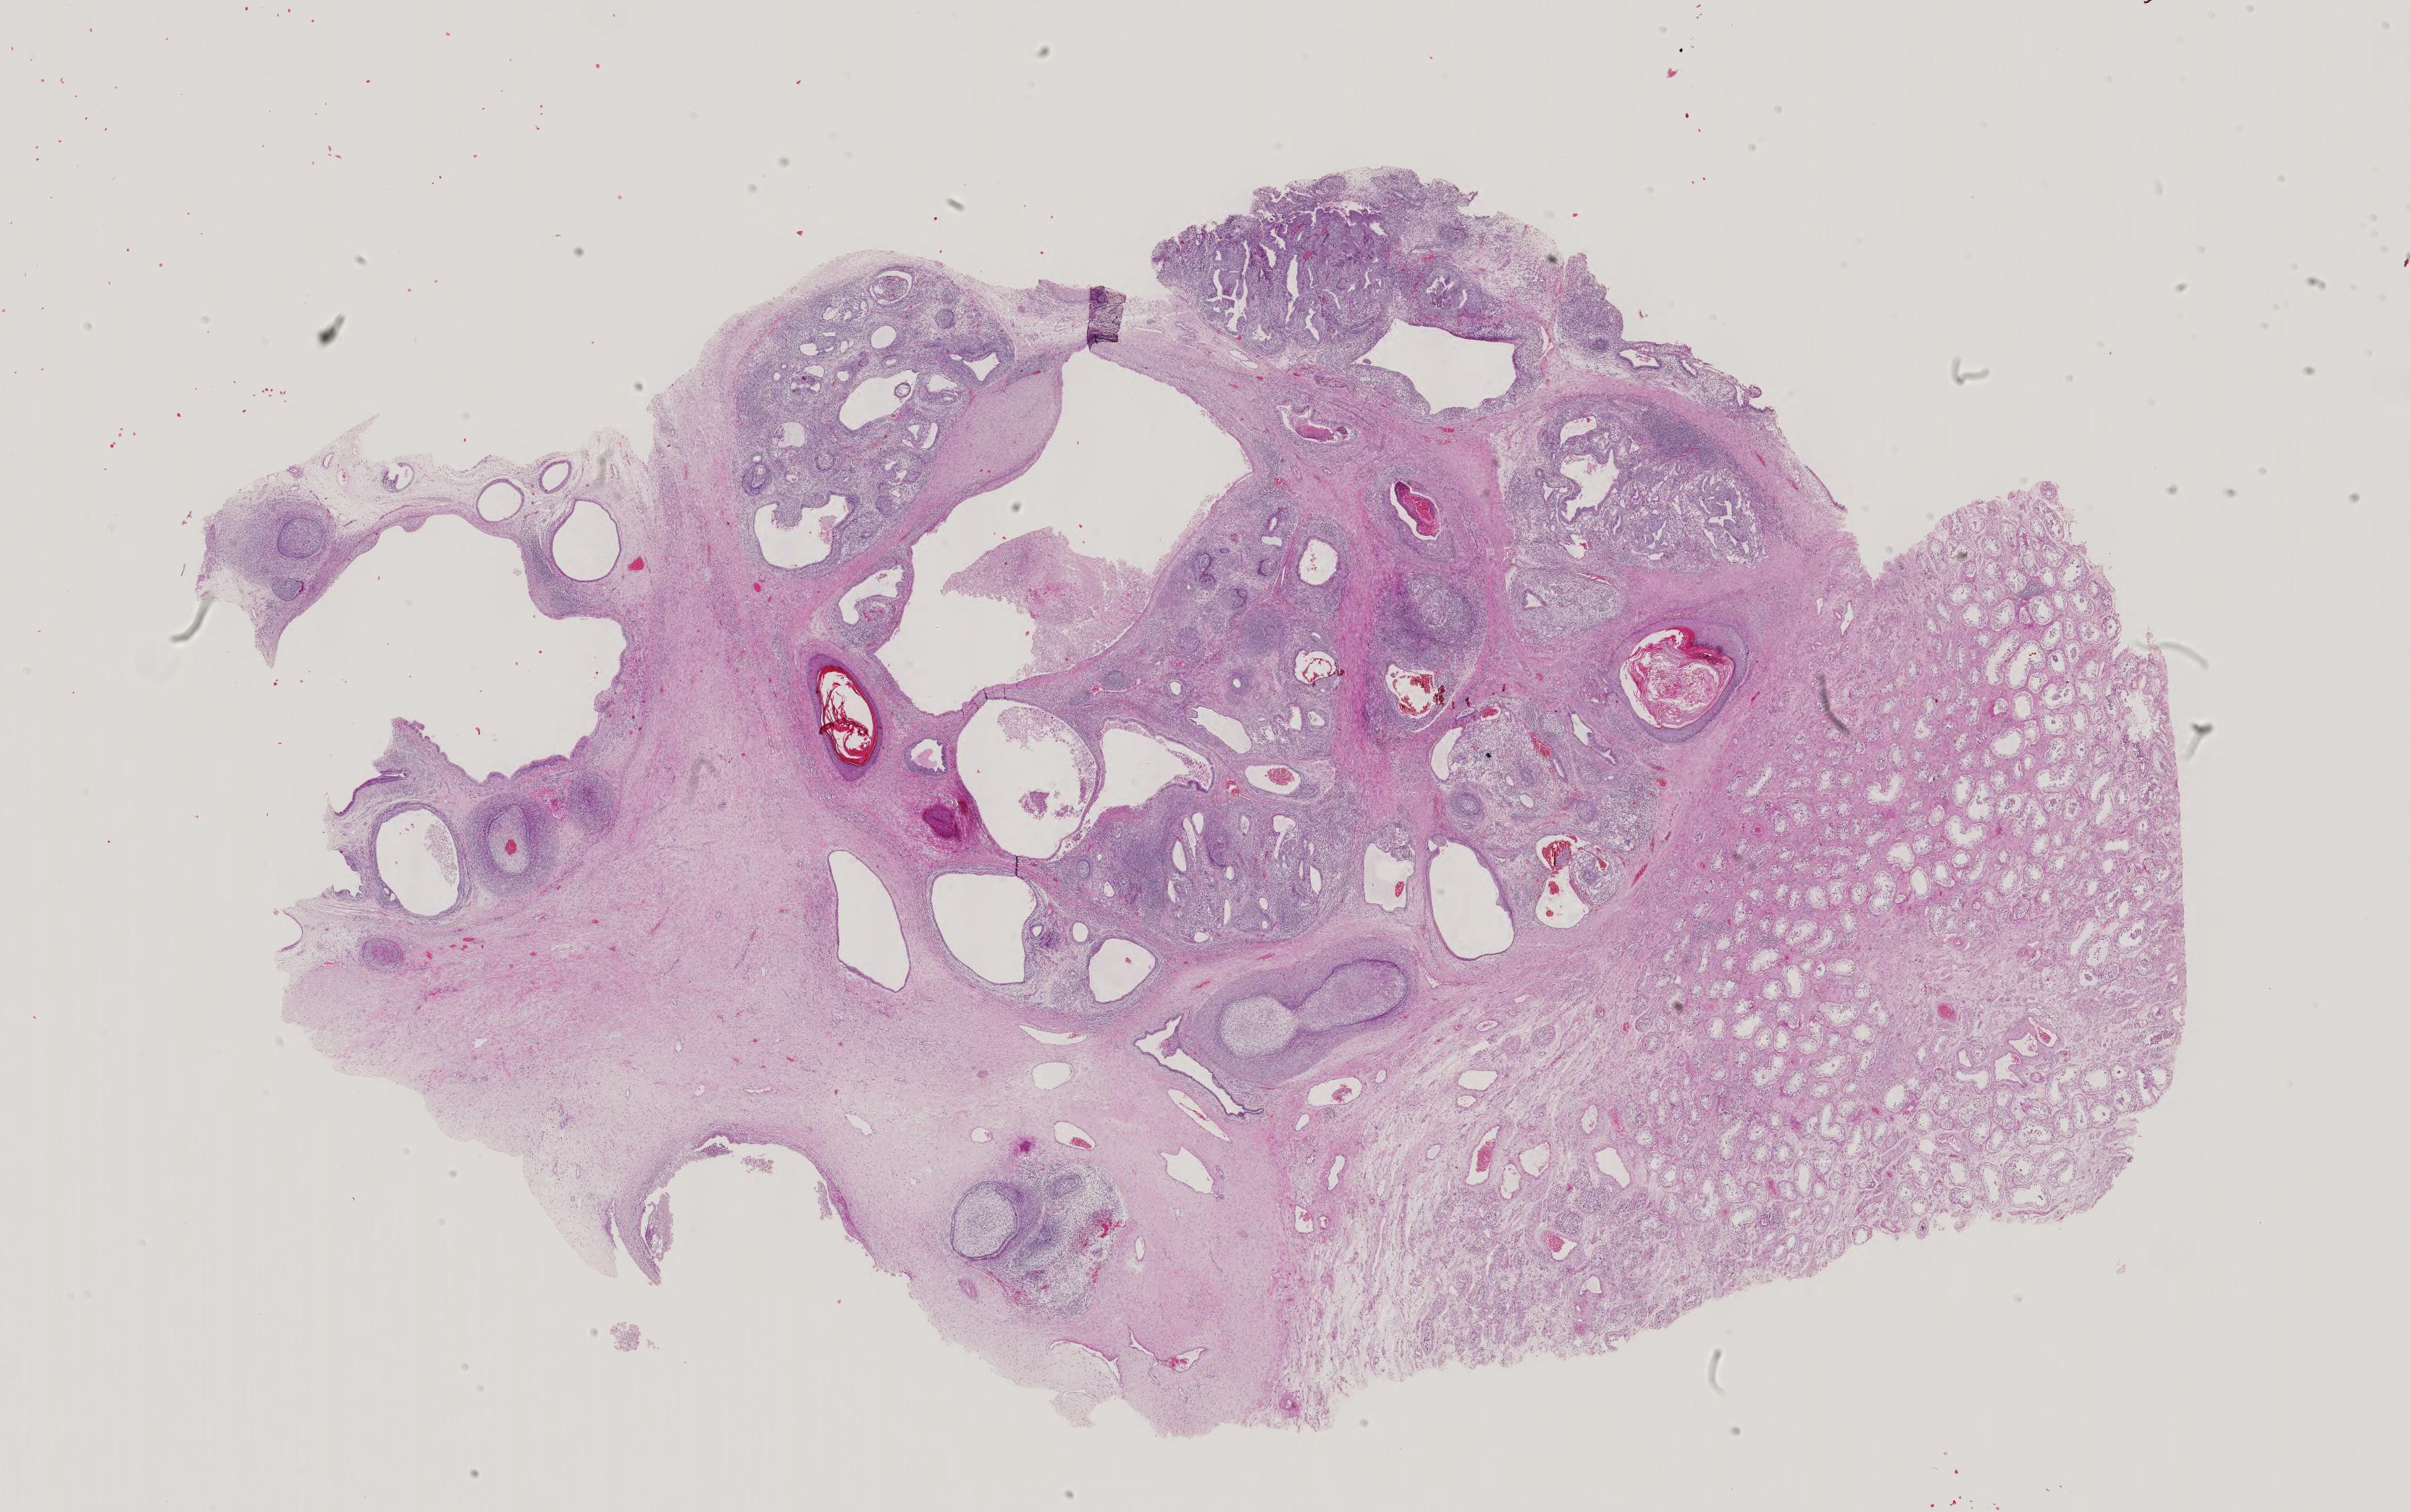
Whole-slide histology image, H&E-stained — low-resolution overview of the scanned area, about 24.2 x 15.2 mm (from a 40x scan). Male patient.
Specimen: formalin-fixed paraffin-embedded (FFPE) diagnostic section; sample: primary tumour, testis.